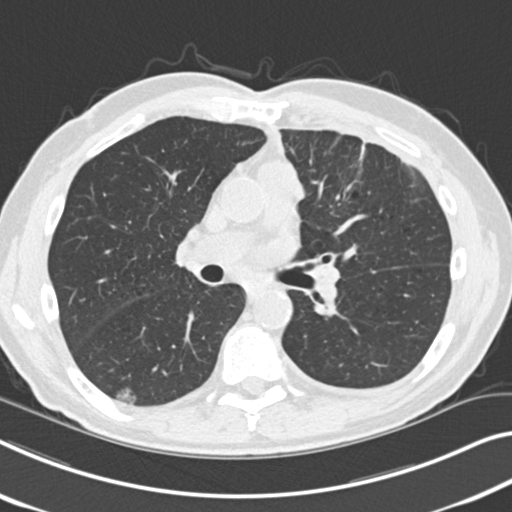
Chest CT (low-dose screening protocol), one axial image; baseline screening round; lung window (W 1500 / L -600 HU); 120 kVp; slice 102 of 212 in the series; 512 × 512 image matrix. Male participant, aged 68 years at enrolment. Current smoker at enrolment.
Expert reader's lesion annotation, box from (x=96, y=378) to (x=147, y=415) px. Screening reader's record for this exam (one nodule recorded; not confirmed to be the boxed lesion): non-calcified nodule or mass ≥4 mm, right lower lobe, 14 × 10 mm, poorly defined margins, ground glass attenuation. Later outcome: lung cancer diagnosed 1018 days after this screen (after the third annual screen) — non-small cell carcinoma, right lower lobe, poorly differentiated (G3), stage IA (AJCC 6th edition), 23 mm at pathology.